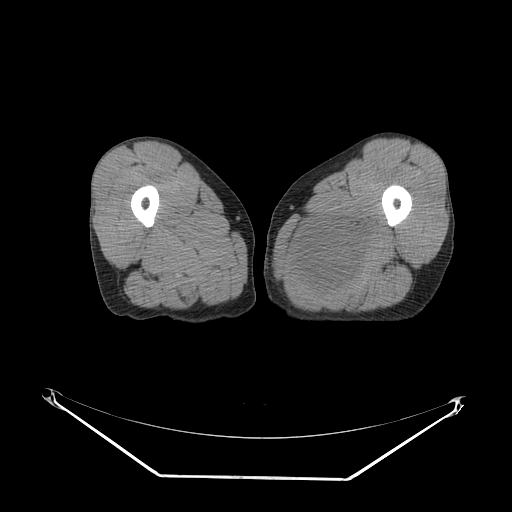
CT of an extremity soft-tissue mass (from a PET/CT study), one axial slice. Position 19 of 267 along the scan axis. Soft-tissue window (W 400 / L 40 HU). 3.75 mm slice thickness. 512 × 512 image matrix. Male patient. Case-level facts recorded for this patient, not image findings: histological type: pleiomorphic liposarcoma; grade: high; site of the primary tumour: left thigh.
Structures marked on this image (expert contour drawn on MRI and transferred to this co-registered scan by the dataset authors):
- gross tumour volume including surrounding oedema: bounding box <295,208,382,298> (left, top, right, bottom; pixels)
- gross tumour volume (mass): <301,224,368,293>